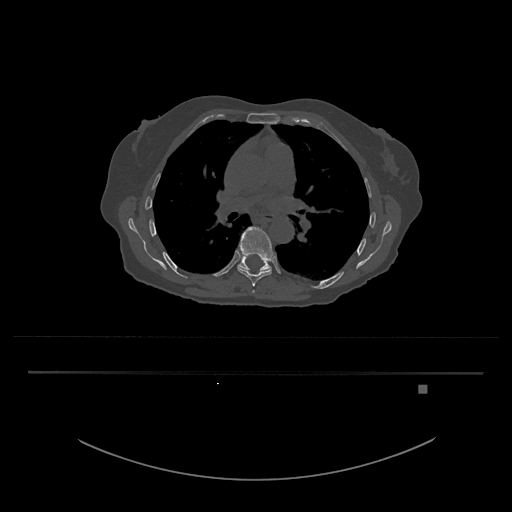
CT including the spine, one axial slice; position 791 of 797 along the scan axis; reconstruction kernel Br40s/3; 120 kVp; bone window (W 1800 / L 400 HU); 512 × 512 image matrix, field of view 500 × 500 mm. Female patient, age 57 years. From the clinical record (not read from this slice): primary cancer: cervical.
Structures marked on this image (semi-automatic segmentation, software-assisted and operator-edited):
- T8 vertebra: bounding box (x1, y1, x2, y2) in pixels: (237, 226, 277, 287)
- T9 vertebra: (238, 256, 272, 272)